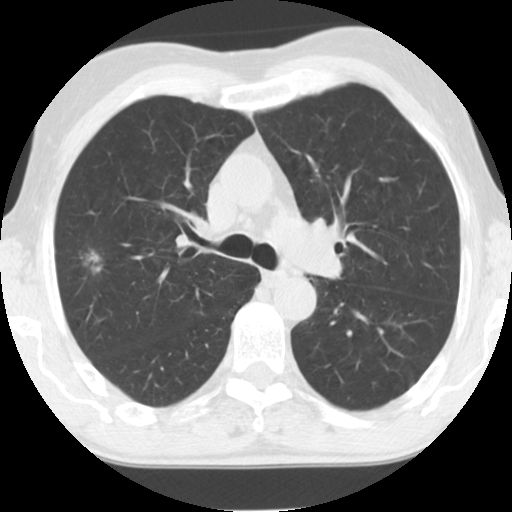
Low-dose screening chest CT, one axial slice. Slice 84 of 124 in the series (ordered by position). Reconstruction kernel STANDARD. Lung window (W 1500 / L -600 HU). 2.5 mm slice thickness. 512 × 512 image matrix, field of view 310 × 310 mm.
Annotated regions visible in this slice (expert manual segmentation):
- lesion 1 (tumor, upper lobe of right lung): bounding box [x1, y1, x2, y2] px = [87, 251, 101, 272]